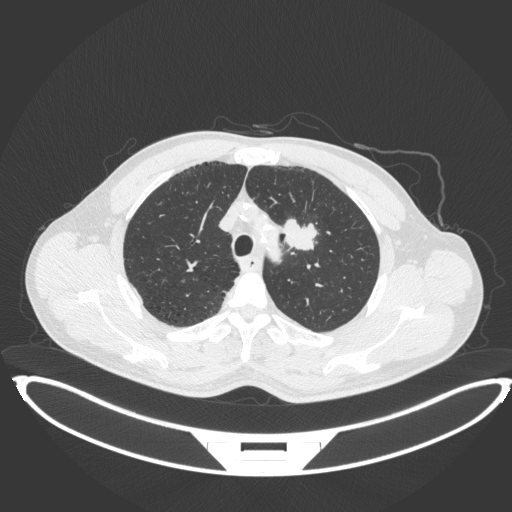
Chest CT, one axial slice; slice 340 of 407 in the series (ordered by position); lung window (W 1500 / L -600 HU); 1 mm slice thickness; 512 × 512 image matrix, field of view 457 × 457 mm. Patient: male, 60 years. Case-level facts recorded for this patient, not image findings: clinical TNM (as recorded): T2a N0 M0.
Structures marked on this image (bounding box drawn by a radiologist):
- lung tumour (recorded histology: squamous cell carcinoma): box from (x=279, y=216) to (x=319, y=255) px